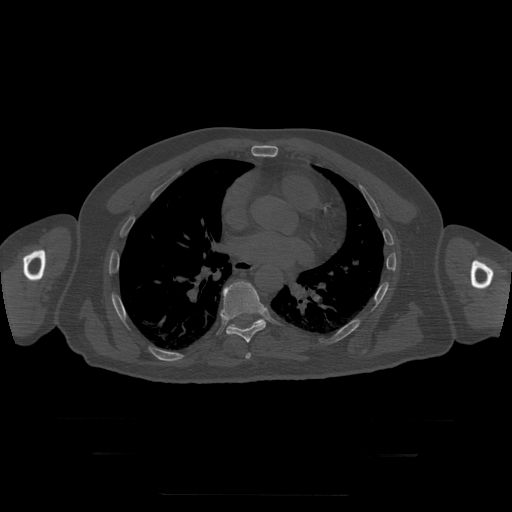
CT including the spine, one axial slice. Slice 163 of 397 in the series (ordered by position). 120 kVp. Bone window (W 1800 / L 400 HU). 1.25 mm slice thickness. 512 × 512 image matrix, field of view 510 × 510 mm. Patient age 73 years. Case-level facts recorded for this patient, not image findings: primary cancer: prostate.
Outlined on this slice (semi-automatically segmented with operator editing):
- T7 vertebra: bounding box <246,353,251,359> (left, top, right, bottom; pixels)
- T8 vertebra: <221,281,266,343>
- T9 vertebra: <231,319,264,328>